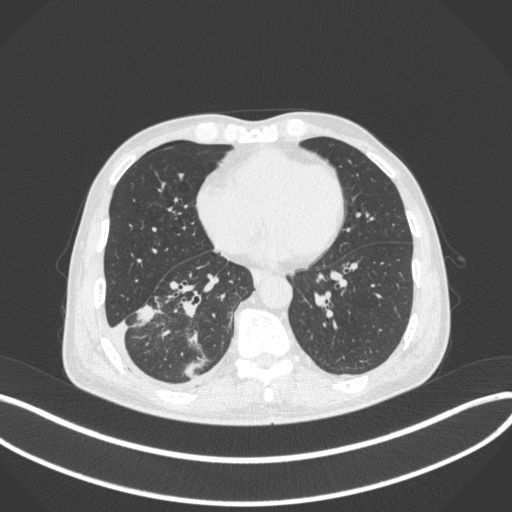
Chest CT, one axial slice; position 146 of 385 along the scan axis; 120 kVp; lung window (W 1500 / L -600 HU); 1 mm slice thickness; 512 × 512 image matrix, field of view 400 × 400 mm. Patient: male, 64 years. Case-level facts recorded for this patient, not image findings: clinical TNM (as recorded): T3 N0 M0; histopathological grade: G2-3.
Outlined on this slice (rectangle marked by the reading radiologist):
- lung tumour (recorded histology: adenocarcinoma): bounding box [x1, y1, x2, y2] px = [131, 296, 159, 329]